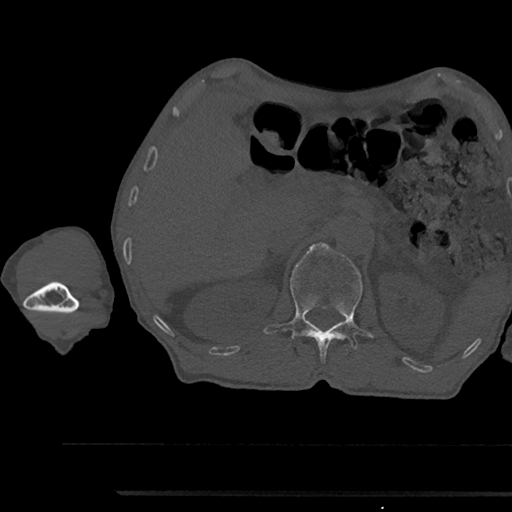
CT including the spine, one axial slice; slice 642 of 797 in the series (ordered by position); 120 kVp; bone window (W 1800 / L 400 HU); 512 × 512 image matrix. Patient: male, 79 years. From the clinical record (not read from this slice): primary cancer: prostate.
Structures marked on this image (semi-automatic segmentation, software-assisted and operator-edited):
- L1 vertebra: bounding box (x1, y1, x2, y2) in pixels: (264, 242, 370, 360)